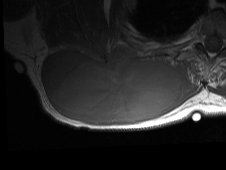
MRI of an extremity soft-tissue mass, one axial slice. Slice 36 of 81 in the series (ordered by position). MR volume resampled by the dataset authors to the PET/CT grid (not the native acquisition matrix). 226 × 170 image matrix. Male patient. Case-level facts recorded for this patient, not image findings: histological type: pleiomorphic spindle cell undifferentiated; grade: high; site of the primary tumour: right parascapusular.
Structures marked on this image (expert contour drawn on MRI and transferred to this co-registered scan by the dataset authors):
- gross tumour volume including surrounding oedema: bounding box [x1, y1, x2, y2] px = [41, 47, 198, 126]
- gross tumour volume (mass): [41, 47, 182, 123]